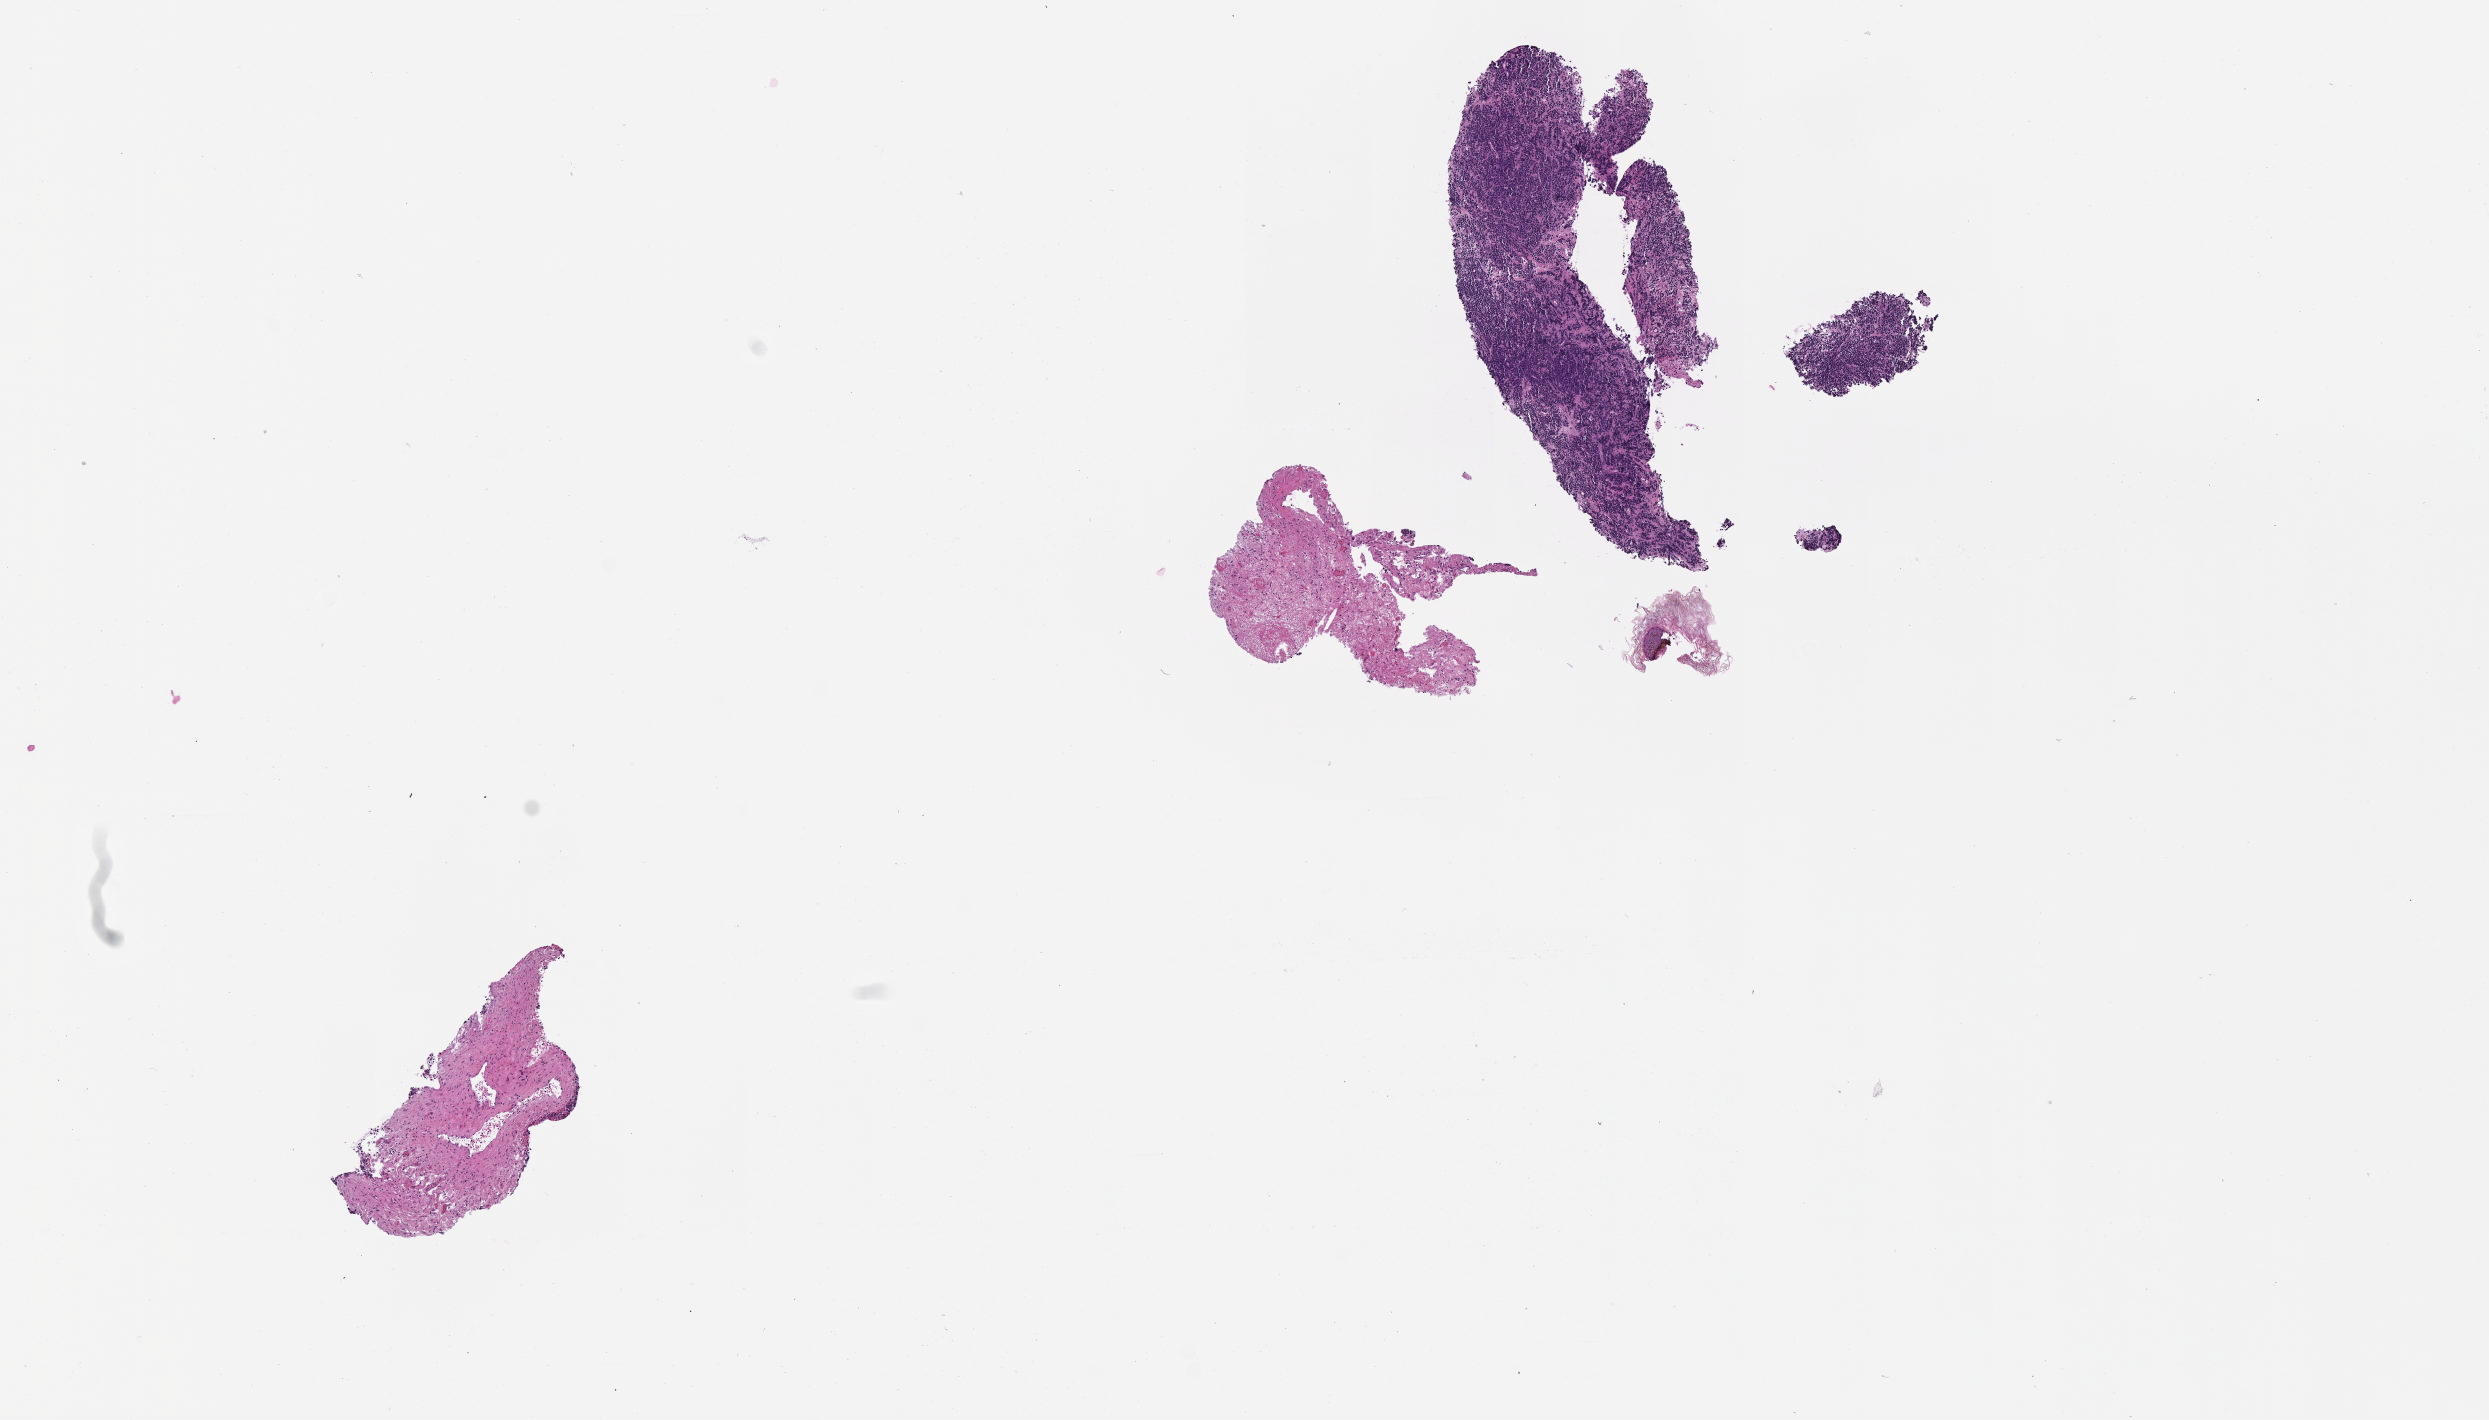
Digitized H&E-stained section — low-resolution overview of the scanned area, about 10.1 x 5.7 mm, specimen: tumor tissue, site: abdomen proper. Female, age 7 years at initial diagnosis.
* histologic diagnosis: Burkitt lymphoma, NOS